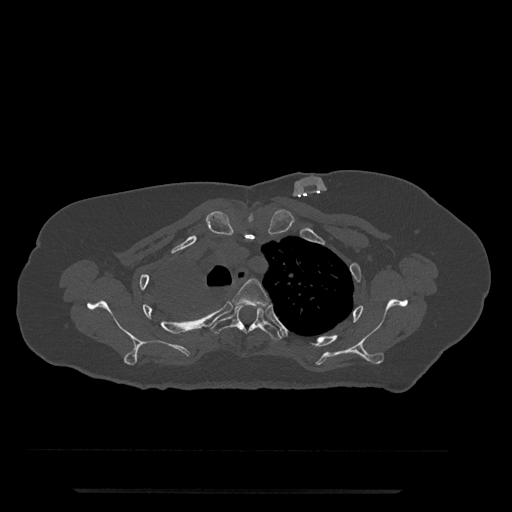
CT including the spine, one axial slice. Position 606 of 797 along the scan axis. 120 kVp. Bone window (W 1800 / L 400 HU). 512 × 512 image matrix, field of view 440 × 440 mm. Female patient, age 51 years. From the clinical record (not read from this slice): primary cancer: neuro; vertebrae with lytic lesions (as recorded): T8.
Structures marked on this image (semi-automatic segmentation, software-assisted and operator-edited):
- T3 vertebra: bounding box (x1, y1, x2, y2) in pixels: (234, 278, 269, 307)
- T4 vertebra: (210, 305, 282, 341)